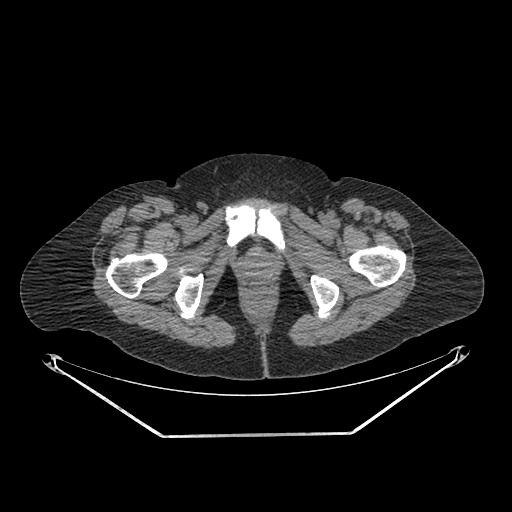
CT of an extremity soft-tissue mass (from a PET/CT study), one axial slice; slice 287 of 311 in the series (ordered by position); reconstruction kernel SOFT; 140 kVp; soft-tissue window (W 400 / L 40 HU); 3.75 mm slice thickness; 512 × 512 image matrix, field of view 500 × 500 mm. Female patient. Case-level facts recorded for this patient, not image findings: histological type: pleiomorphic undifferentiated sarcoma; grade: high; site of the primary tumour: right quadricep.
Annotated regions visible in this slice (expert contour drawn on MRI and transferred to this co-registered scan by the dataset authors):
- tumour plus oedema (research contour): box from (x=110, y=233) to (x=133, y=266) px